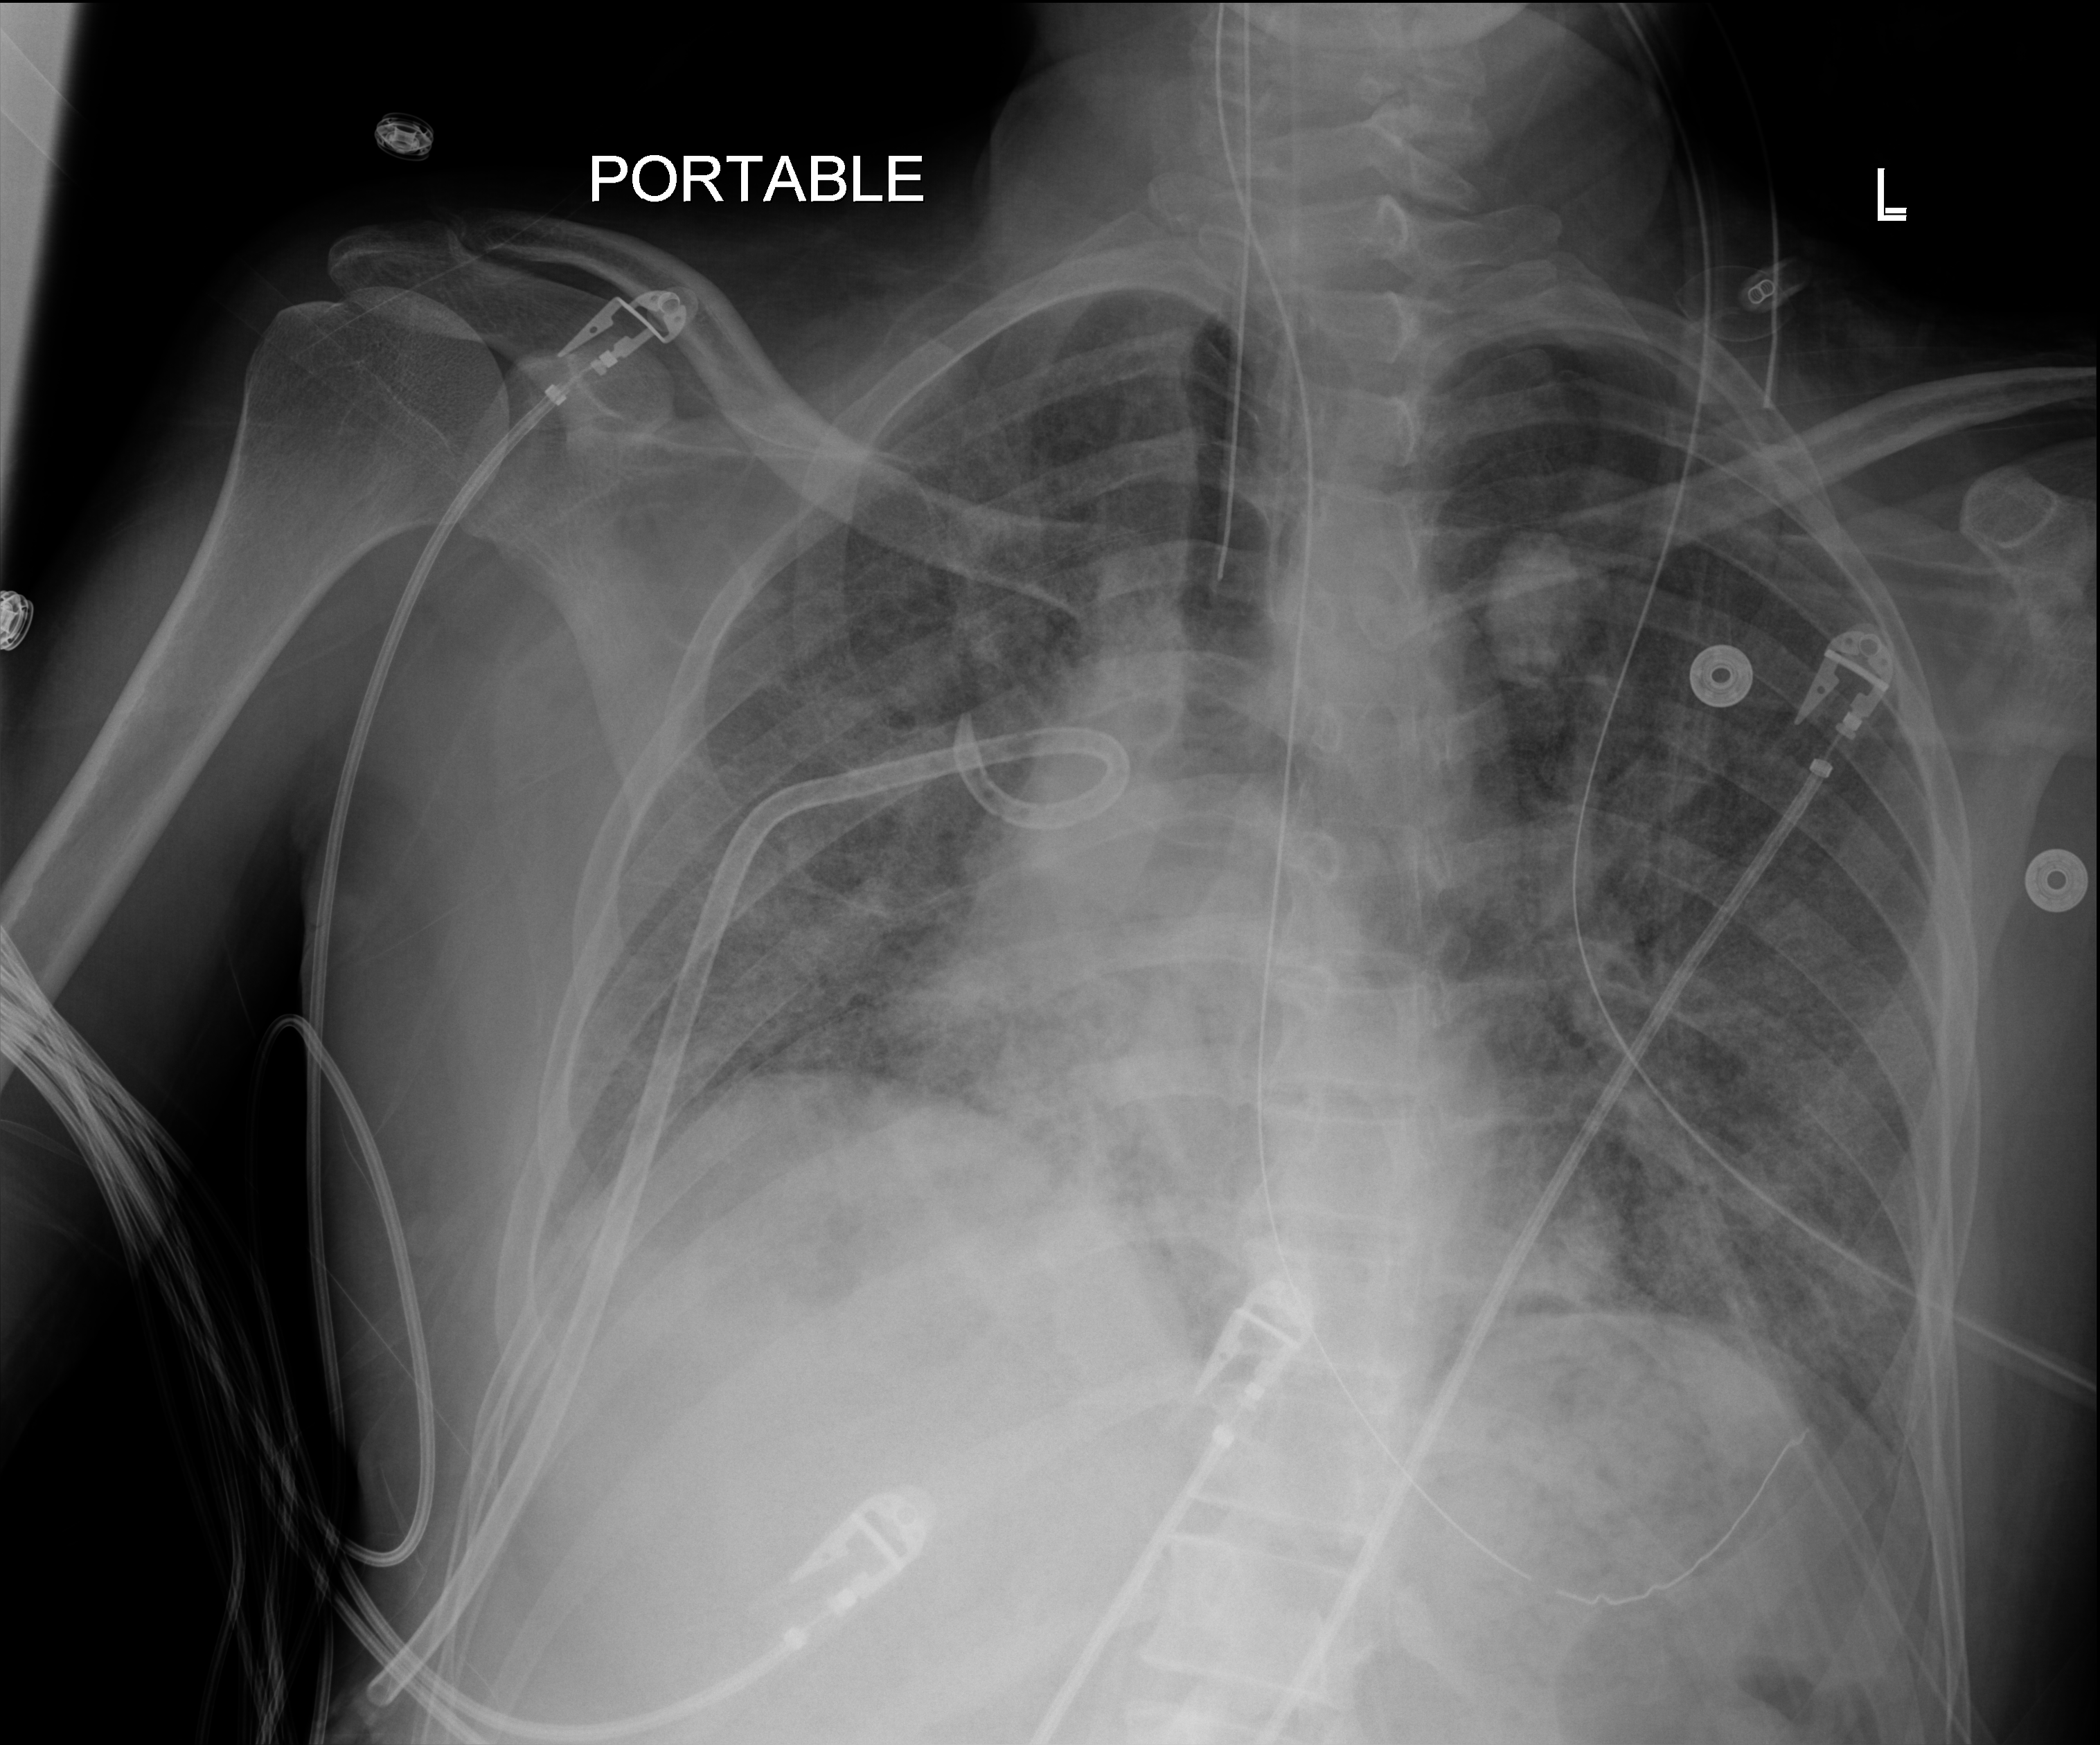
Portable chest radiograph; anteroposterior (AP) projection. Adult patient hospitalised with COVID-19, age 18–59 years.
From the hospital-stay record, not from the radiograph (when in the stay this image was taken is not recorded): admitted to intensive care during this hospital stay: yes.